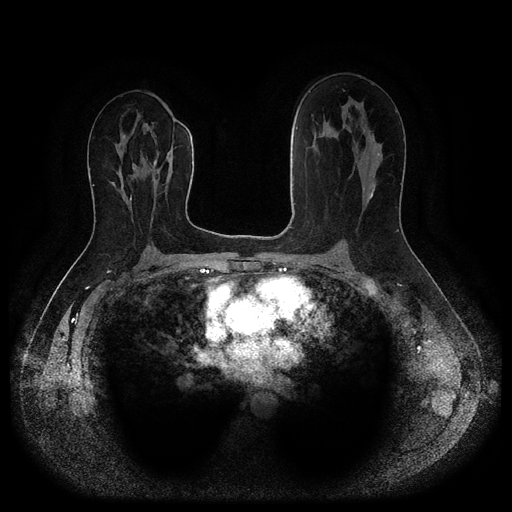
Breast MRI (dynamic contrast-enhanced, multi-phase), one axial slice; slice 56 of 116 in the series (ordered by position); dynamic contrast-enhanced series, time point 2 of 5 at this slice position (early post-contrast); 1.5 T; TE 2.6 ms, TR 5.3 ms; 2.2 mm slice thickness; 512 × 512 image matrix. Patient: female, 53 years.
Structures marked on this image (semi-automatically segmented with operator editing):
- breast lesion (labelled benign in the annotation): box from (x=152, y=159) to (x=157, y=167) px